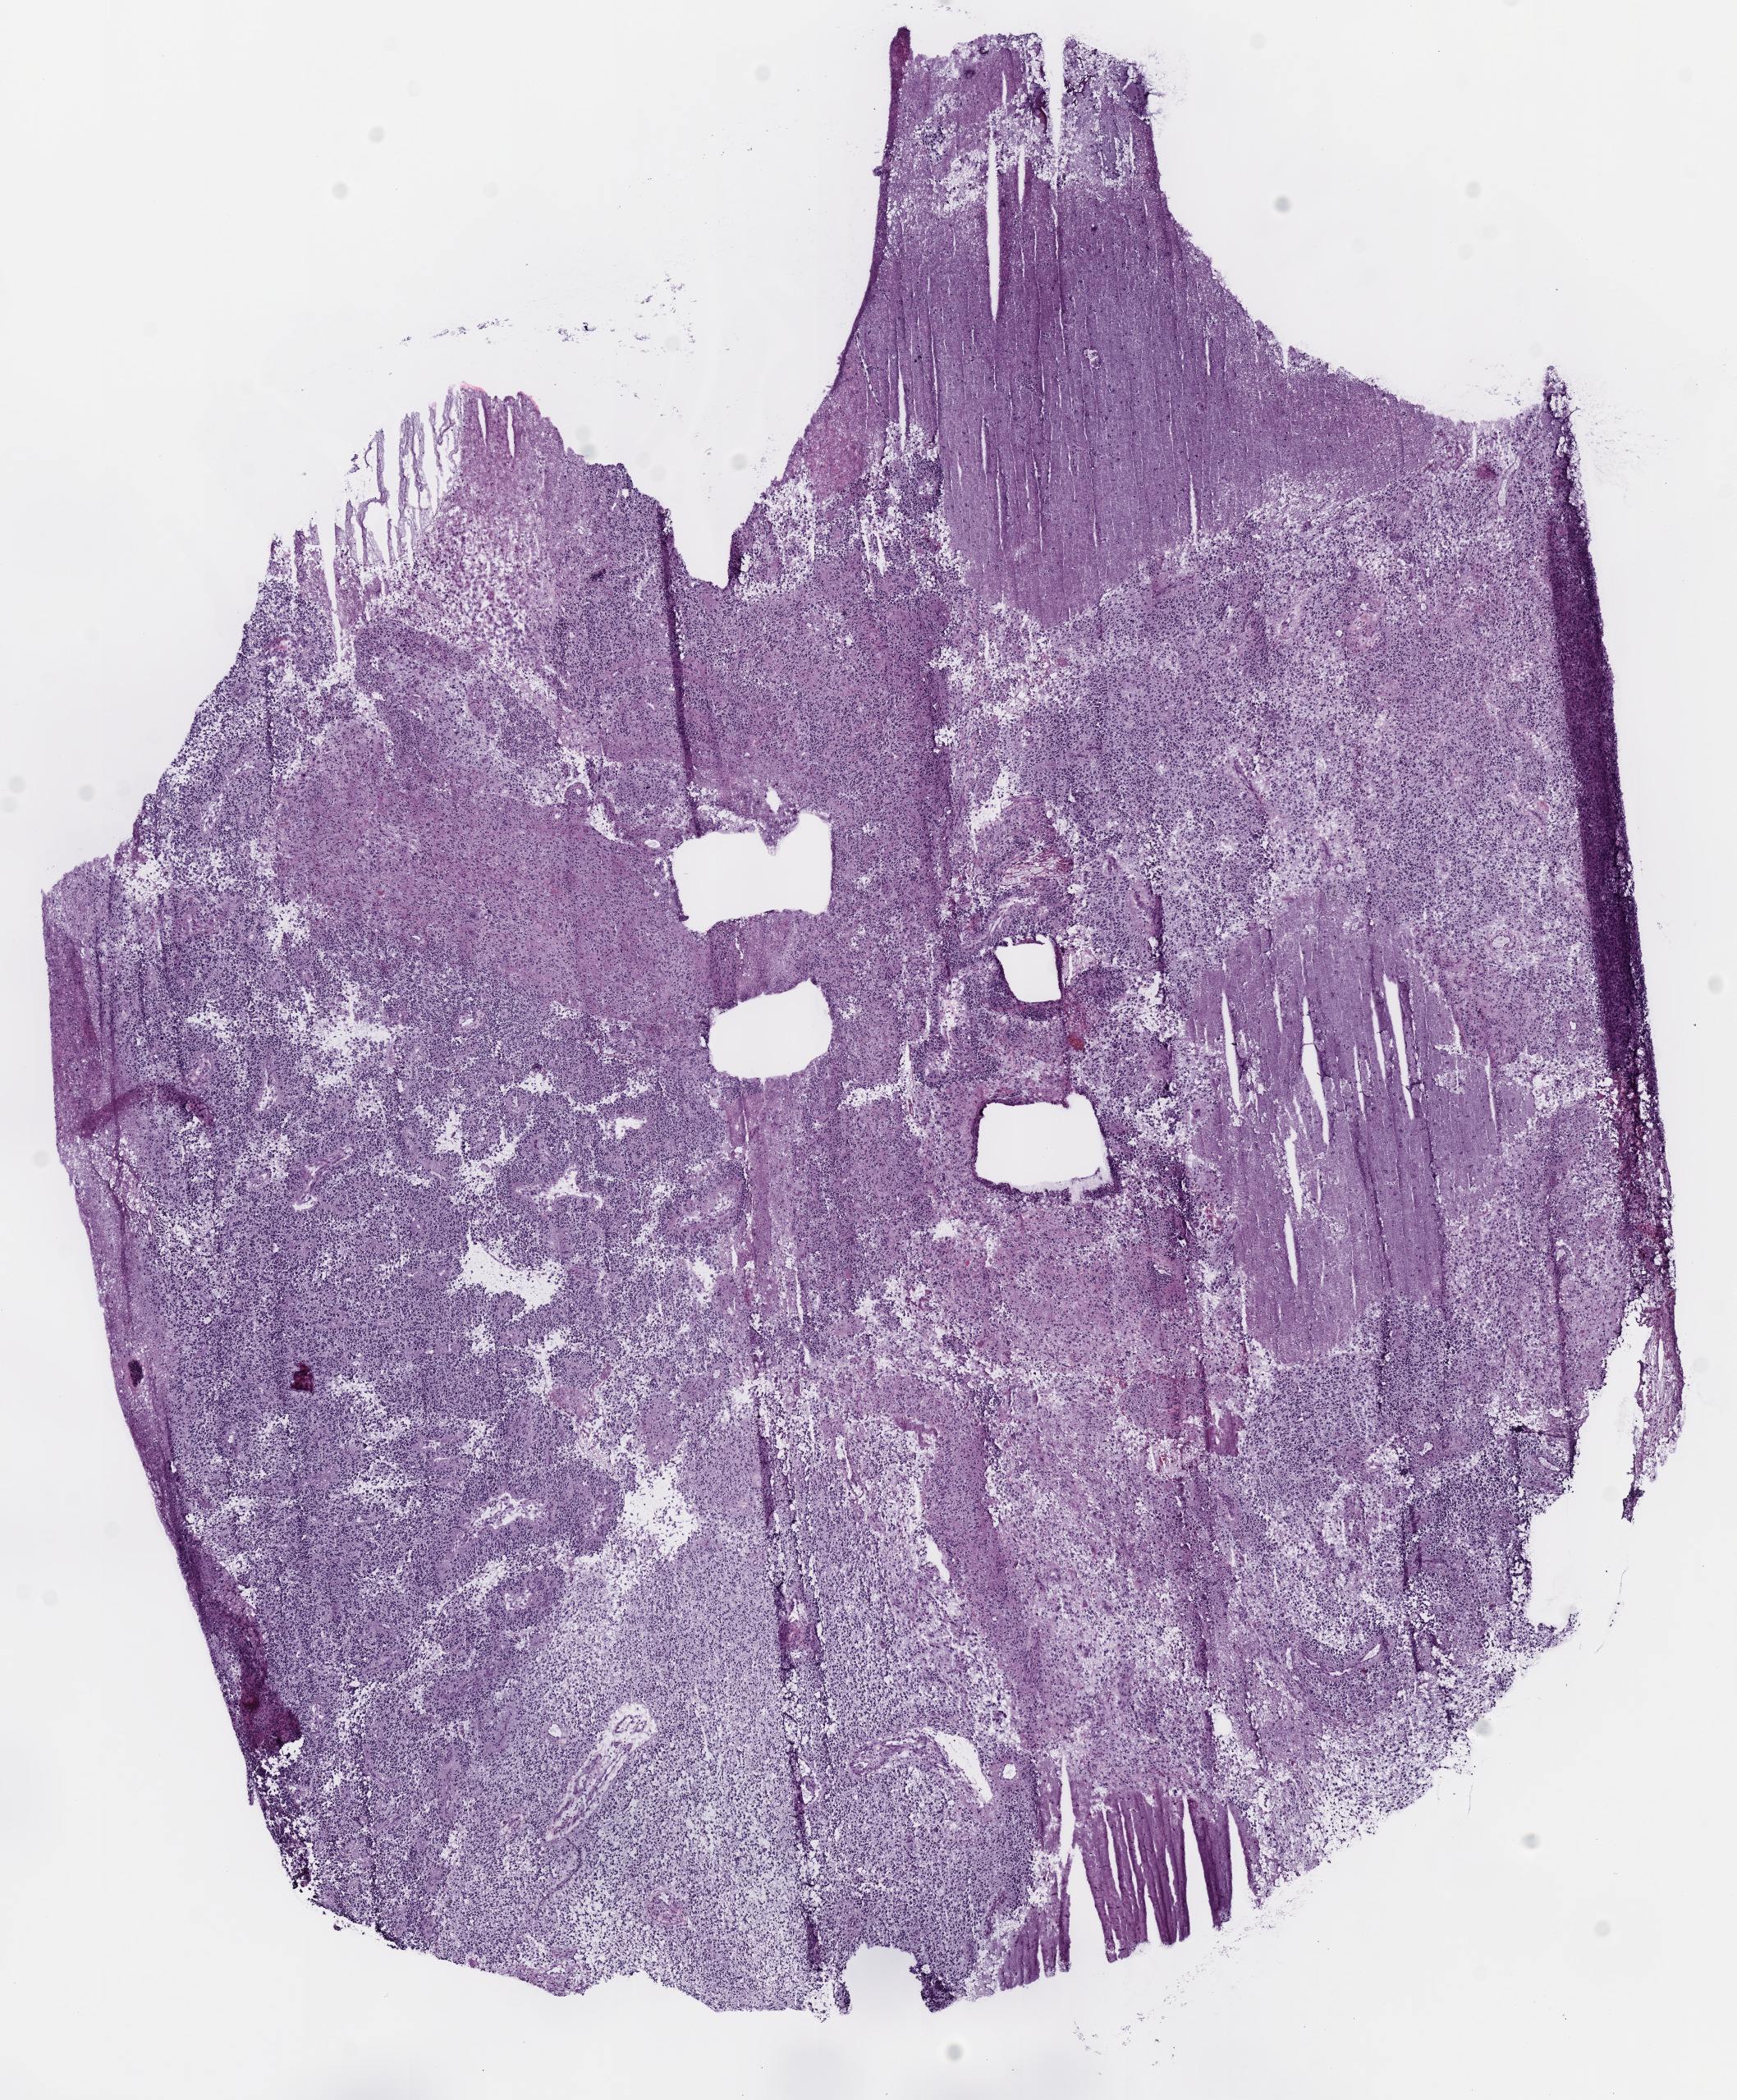
H&E whole-slide image, low-resolution overview of the scanned area, about 8.3 x 10.1 mm (acquisition: 40x scan), frozen section from the top of the tissue portion, sample: primary tumour, brain. Female patient; age at initial diagnosis 60 years. Histologic grade: G3 (poorly differentiated). Pathologist review of this section (percent, as recorded): tumour cells 92%, tumour nuclei 85%, normal cells 8%, stromal cells 0%, necrosis 0%.
• laterality: left
• diagnosis: Oligodendroglioma, NOS (cerebrum)